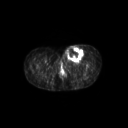
FDG PET of an extremity soft-tissue mass (from a PET/CT study), one axial slice; 3.27 mm slice thickness; 128 × 128 image matrix, field of view 600 × 600 mm. Female patient, age 24 years. From the clinical record (not read from this slice): histological type: leiomyosarcoma; grade: high; site of the primary tumour: groin.
Outlined on this slice (expert contour drawn on MRI and transferred to this co-registered scan by the dataset authors):
- gross tumour volume including surrounding oedema: bounding box (x1, y1, x2, y2) in pixels: (62, 44, 84, 62)
- gross tumour volume (mass): (67, 45, 84, 61)